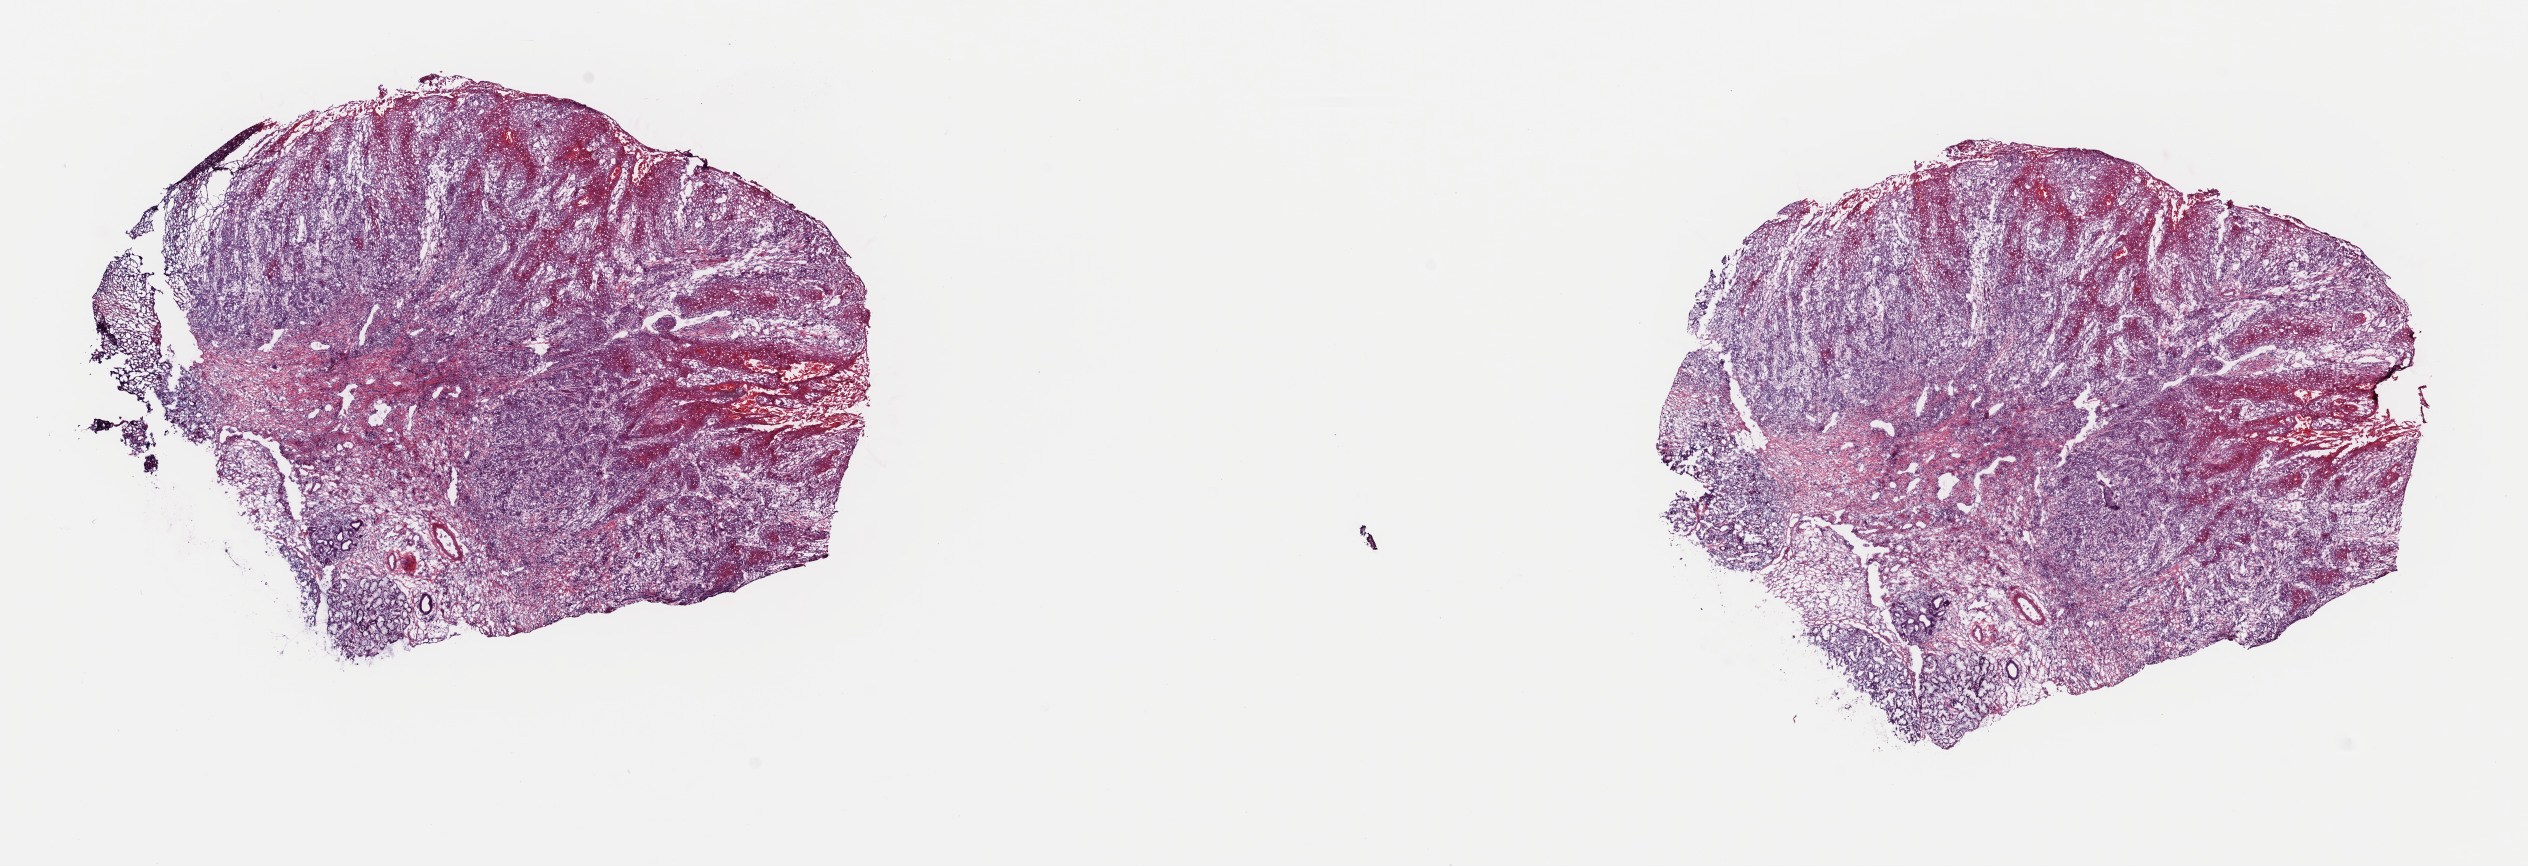
Digitized H&E tissue section (whole slide), whole scanned area (about 20.0 x 6.8 mm, from a 40x scan) shown as a low-resolution overview, frozen section, sample: primary tumour, head and neck. Male, age 55 years at initial diagnosis. Slide review estimates, as recorded: tumour cells 65%, tumour nuclei 80%.
Pathologic diagnosis: Squamous cell carcinoma, NOS (floor of mouth, NOS).